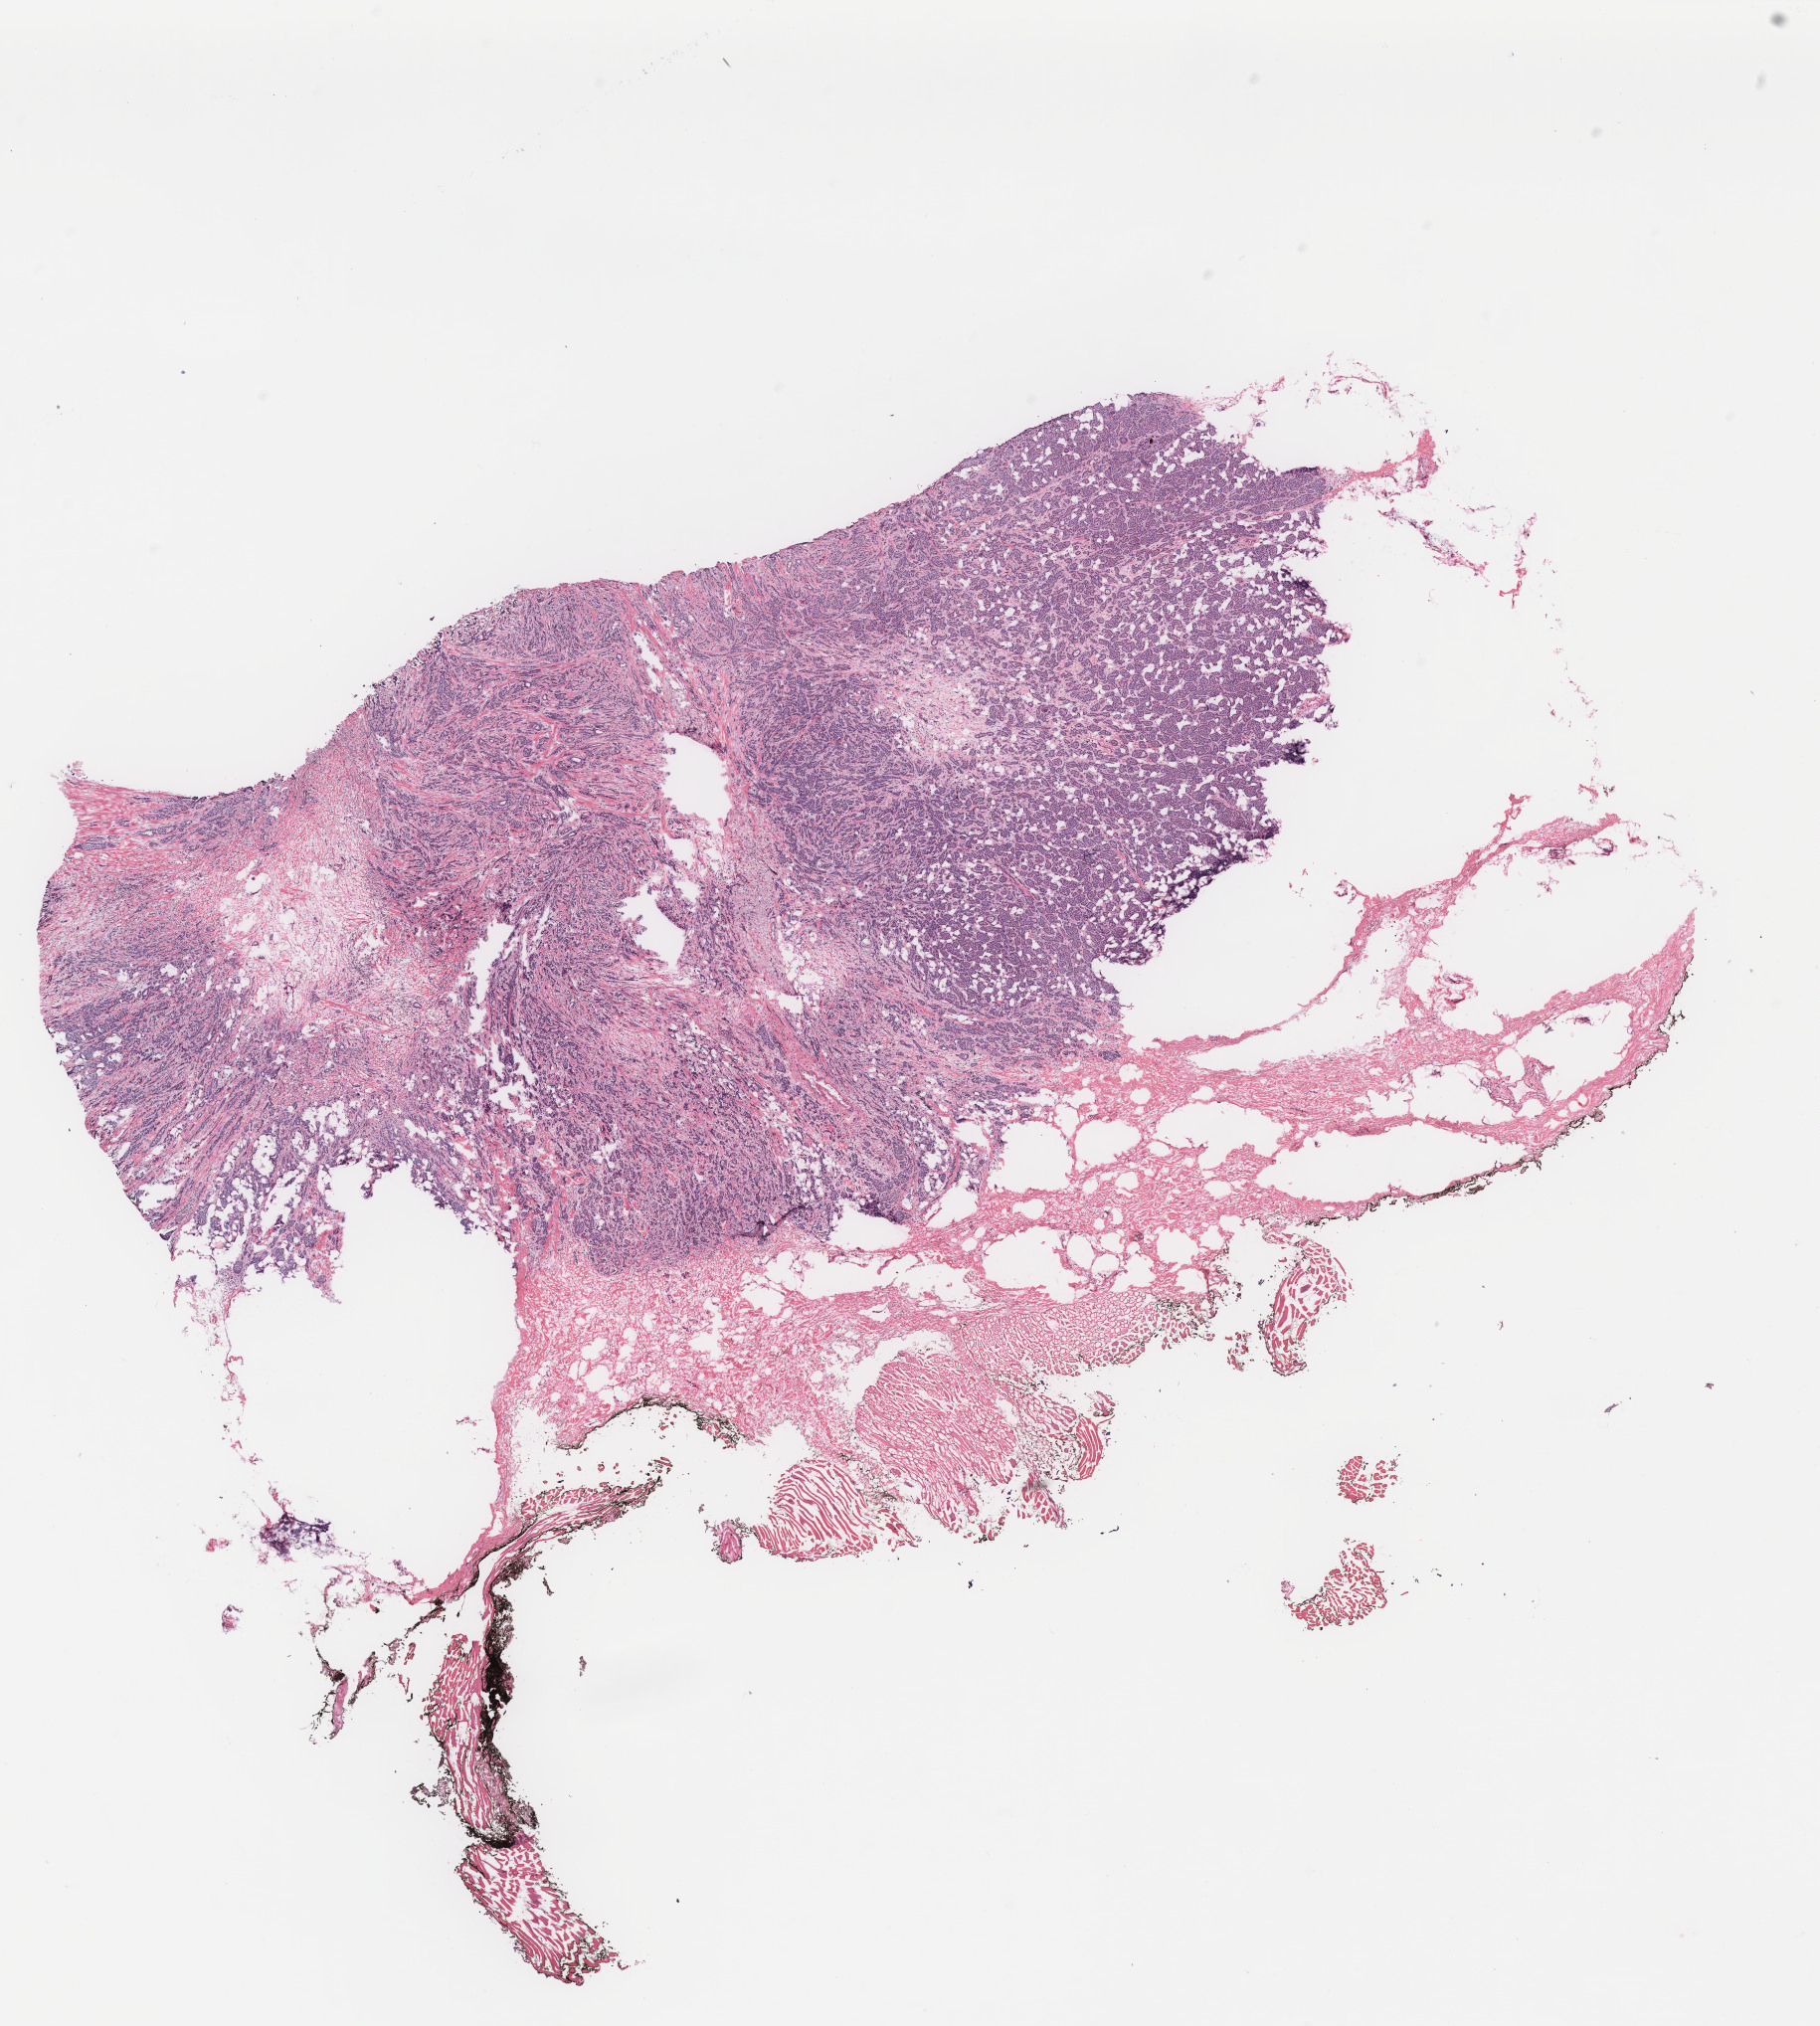
Hematoxylin and eosin (H&E) stained whole-slide image — a low-resolution overview of the entire scanned area, about 14.6 x 16.3 mm, breast, tissue type not recorded. Patient: female, age 50 years.
• patient diagnosis: Infiltrating duct carcinoma, NOS